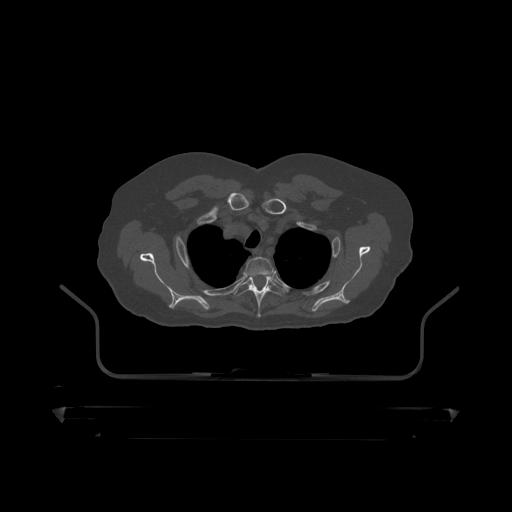
CT including the spine, one axial slice; position 364 of 390 along the scan axis; reconstruction kernel STANDARD; bone window (W 1800 / L 400 HU); 1.25 mm slice thickness; 512 × 512 image matrix, field of view 650 × 650 mm. Patient: male, 60 years. From the clinical record (not read from this slice): primary cancer: prostate.
Outlined on this slice (semi-automatically segmented with operator editing):
- T2 vertebra: bounding box [x1, y1, x2, y2] px = [244, 257, 274, 277]
- T3 vertebra: [234, 276, 285, 319]